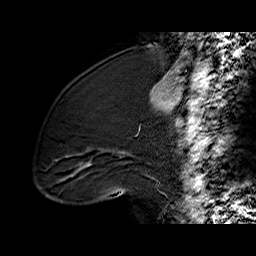
Breast MRI (dynamic contrast-enhanced), one sagittal slice; position 23 of 60 along the scan axis; dynamic contrast-enhanced series, time point 2 of 6 at this slice position (early post-contrast); 1.5 T; TE 6.2 ms, TR 32.4 ms; 4 mm slice thickness; 256 × 256 image matrix. Female patient. From the clinical record (not read from this slice): setting: breast cancer imaged before/during neoadjuvant chemotherapy; receptor status: triple-negative.
Structures marked on this image (semi-automatically segmented with operator editing):
- analysis volume of interest (the breast-tissue region the enhancement analysis was run in; not a lesion): box from (x=37, y=100) to (x=134, y=196) px
- tumour enhancement mask (voxels above the 100 % enhancement threshold inside the analysis volume of interest): (x=120, y=151)–(x=124, y=153)